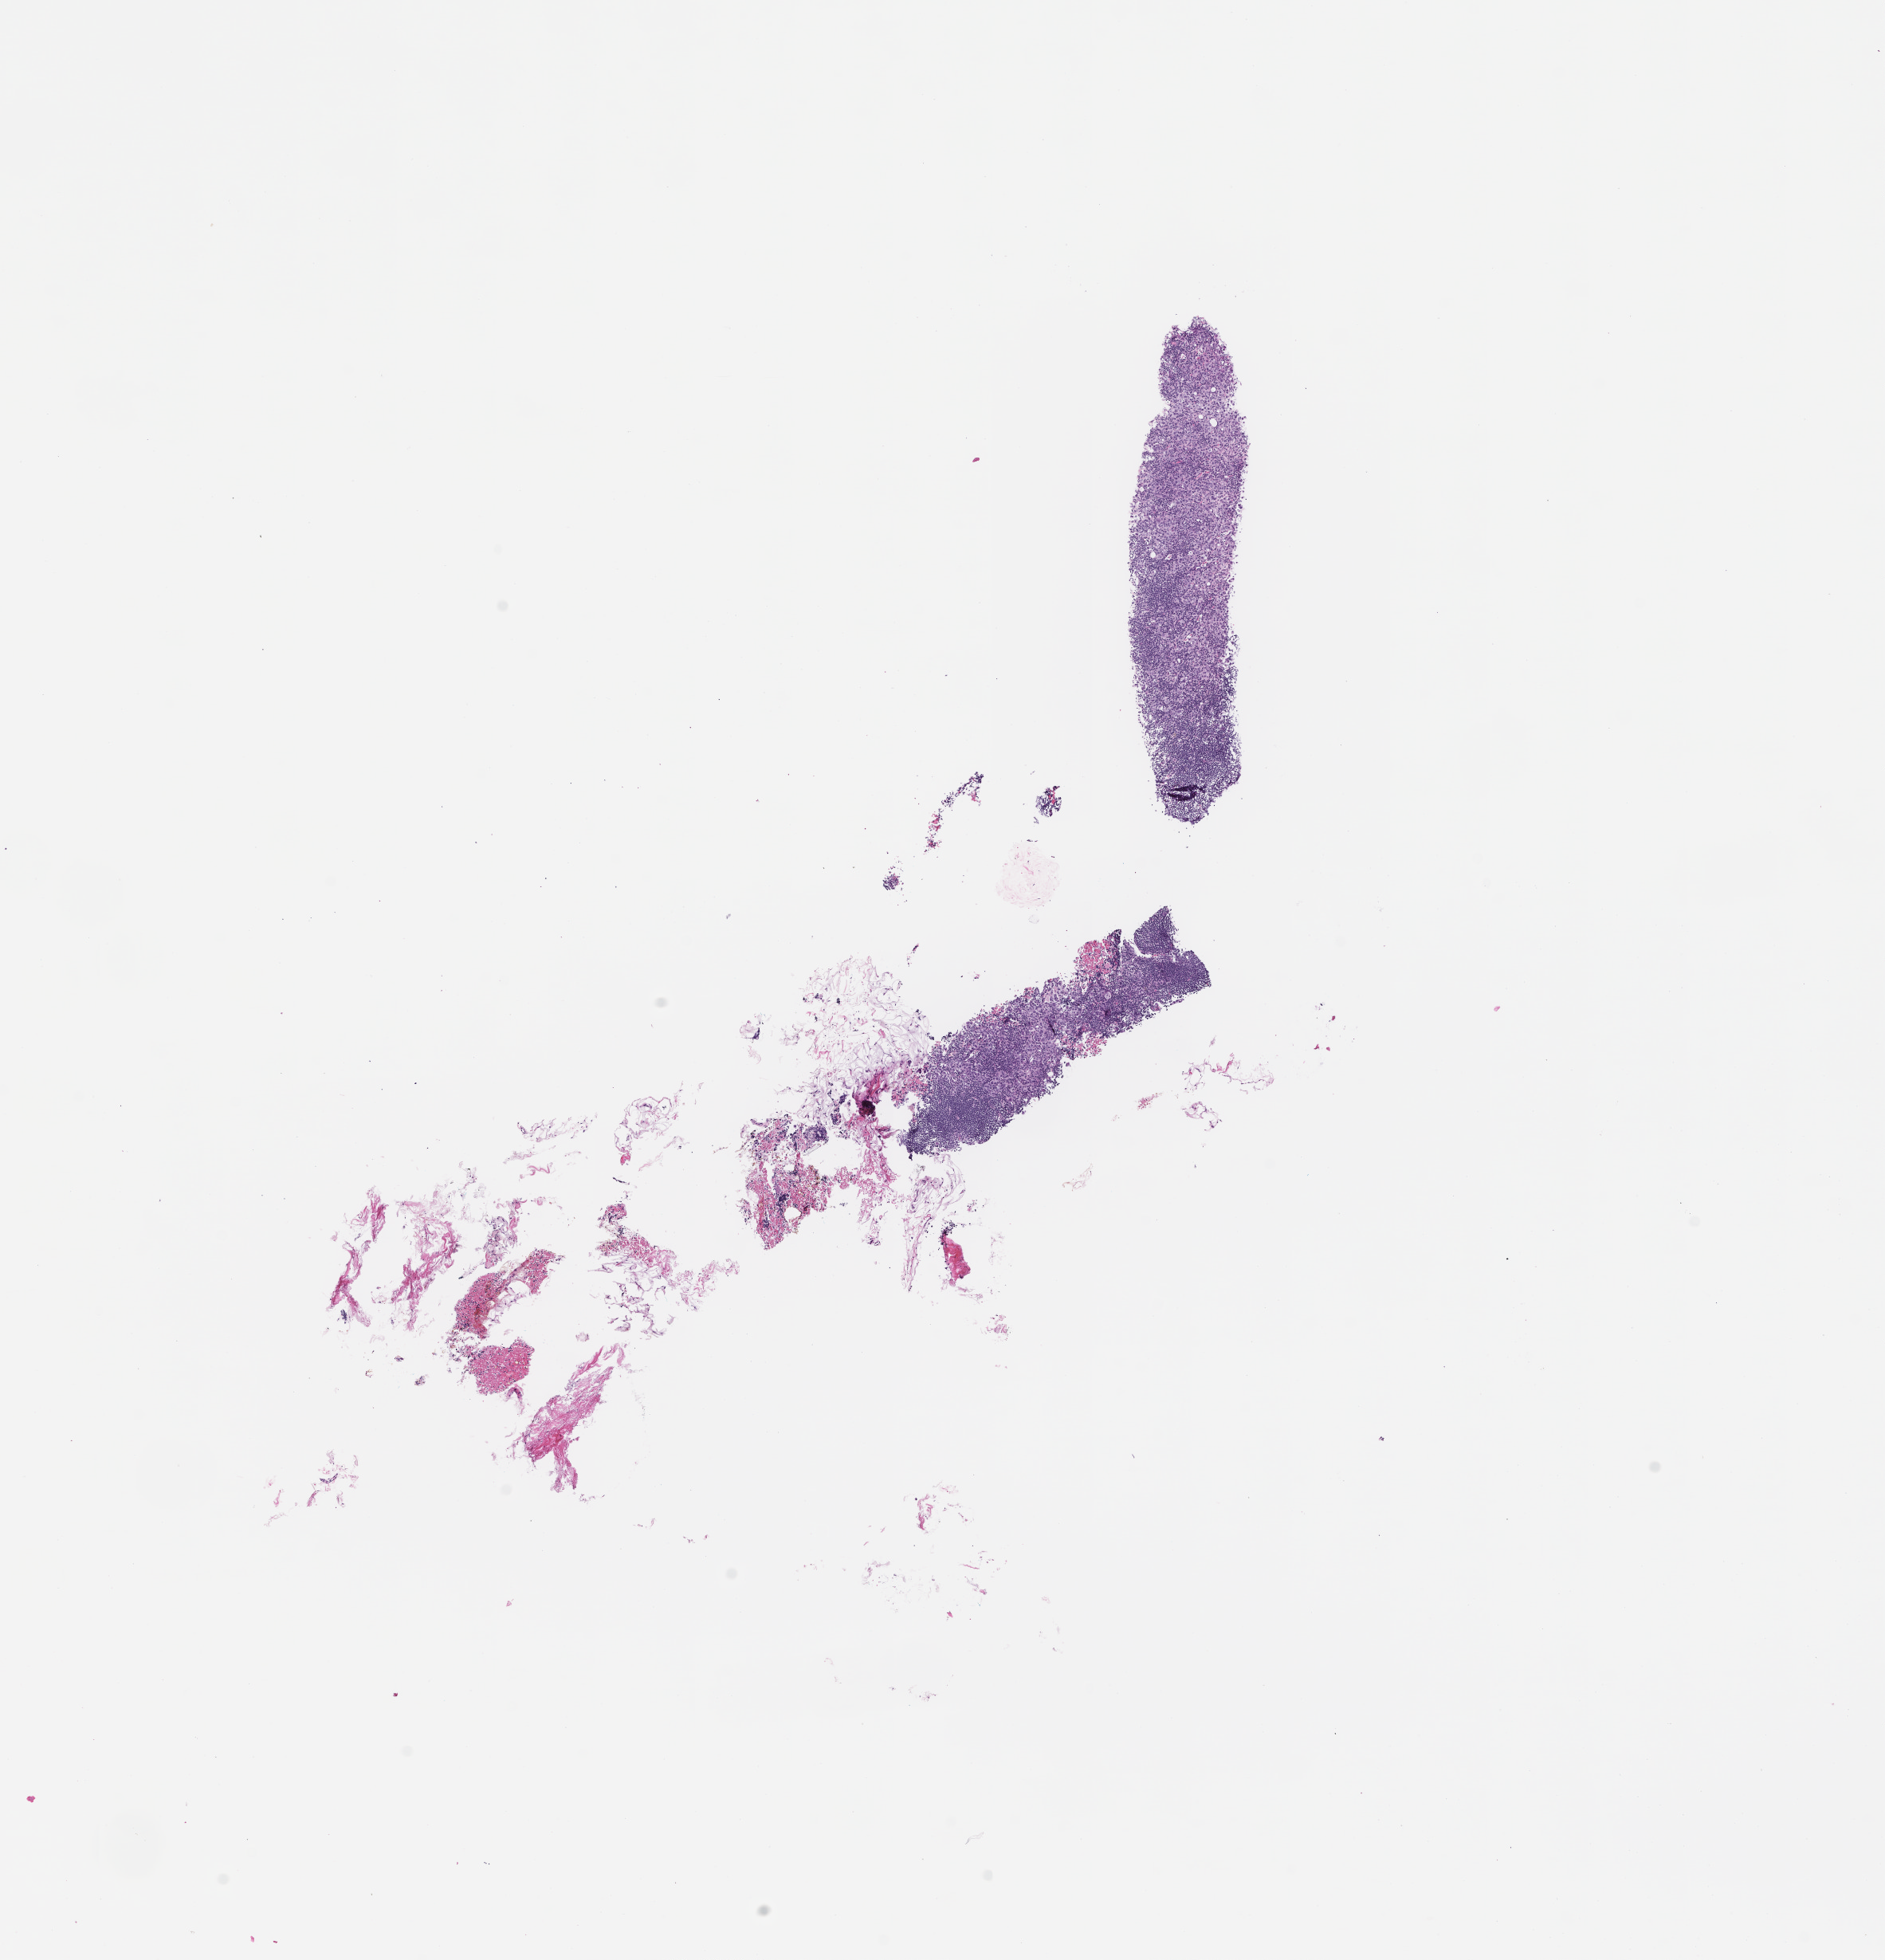
Digitized H&E-stained section — whole scanned area (about 9.5 x 9.9 mm) shown as a low-resolution overview; FFPE section; site: breast; specimen time point: archival tissue. Patient: female.
- this section: primary tumour tissue
- diagnosis: Invasive Breast Carcinoma